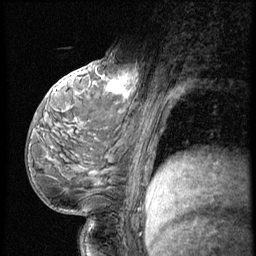
Breast MRI (dynamic contrast-enhanced), one sagittal slice. Slice 33 of 56 in the series (ordered by position). 3 images stored at this slice position (order not interpretable as contrast timing). 1.5 T. TE 4.2 ms, TR 9 ms. 2.5 mm slice thickness. 256 × 256 image matrix, field of view 180 × 180 mm. Patient: female, 54 years. Case-level facts recorded for this patient, not image findings: setting: breast cancer imaged before/during neoadjuvant chemotherapy; receptor status: triple-negative.
Annotated regions visible in this slice (semi-automatic segmentation, software-assisted and operator-edited):
- analysis volume of interest (the breast-tissue region the enhancement analysis was run in; not a lesion): box from (x=99, y=53) to (x=149, y=102) px
- tumour enhancement mask (voxels above the 140 % enhancement threshold inside the analysis volume of interest): (x=109, y=68)–(x=140, y=95)